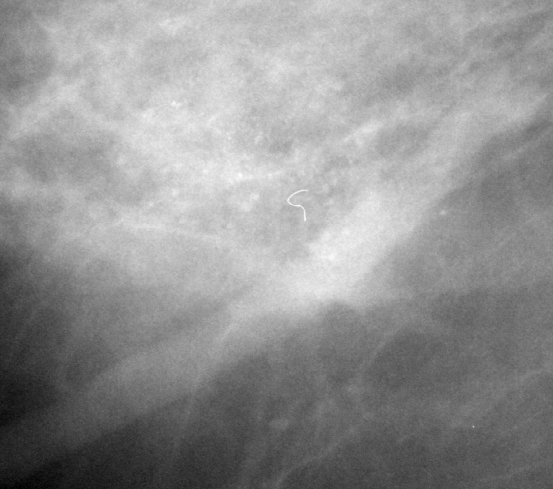
Cropped region of a digitized screen-film mammogram centred on a radiologist-marked abnormality, right breast, MLO view, BI-RADS breast density category 2 (scale 1–4).
Finding: calcifications, morphology amorphous, distribution clustered; BI-RADS assessment category 4; pathology result (as recorded, not read from the image): benign.